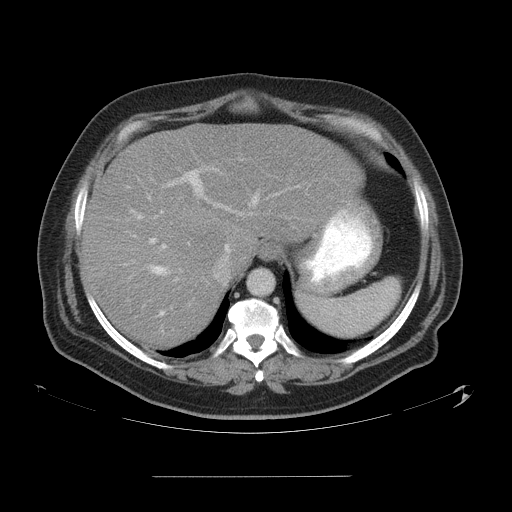
Contrast-enhanced abdominal CT, one axial slice; position 42 of 58 along the scan axis; 120 kVp; intravenous contrast given; soft-tissue window (W 400 / L 40 HU); 5 mm slice thickness; 512 × 512 image matrix, field of view 480 × 480 mm. Male patient, age 63 years. Case-level facts recorded for this patient, not image findings: diagnosis: colorectal cancer liver metastases, imaged before liver resection; multiple liver metastases: no; largest metastasis: 4.2 cm; disease in both lobes: no.
Outlined on this slice (outlined manually by an expert reader):
- hepatic veins: bounding box (x1, y1, x2, y2) in pixels: (131, 179, 300, 316)
- liver: (83, 124, 357, 347)
- planned liver remnant (the part of the liver to remain after resection): (83, 197, 222, 347)
- portal vein (with intrahepatic branches): (125, 159, 245, 309)